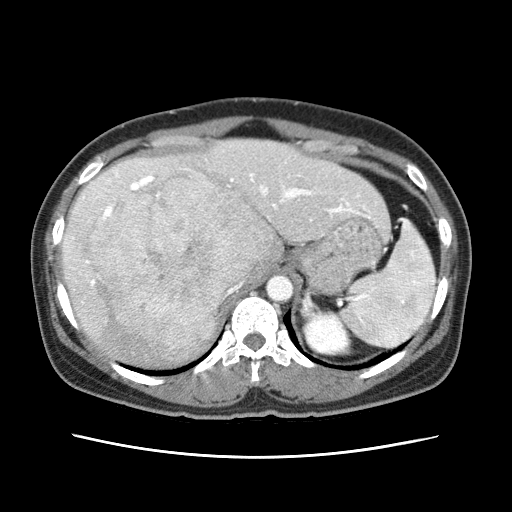
Contrast-enhanced abdominal CT (liver protocol), one axial slice. Slice 46 of 79 in the series (ordered by position). Reconstruction kernel STANDARD. 120 kVp. Soft-tissue window (W 400 / L 40 HU). 2.5 mm slice thickness. 512 × 512 image matrix, field of view 340 × 340 mm. Case-level facts recorded for this patient, not image findings: diagnosis: hepatocellular carcinoma (patient treated with transarterial chemoembolisation; whether this scan precedes or follows treatment is not stated here); TNM stage (as recorded): Stage-I; Child-Pugh class: A; tumour differentiation: moderately differentiated.
Structures marked on this image (semi-automatically segmented with operator editing):
- abdominal aorta: bounding box (x1, y1, x2, y2) in pixels: (266, 275, 294, 301)
- liver parenchyma outside the tumour (the mass and vessels are separate outlines, so this box may not span the whole liver): (62, 140, 376, 366)
- mass: (95, 179, 276, 348)
- liver vessels: (73, 173, 349, 285)